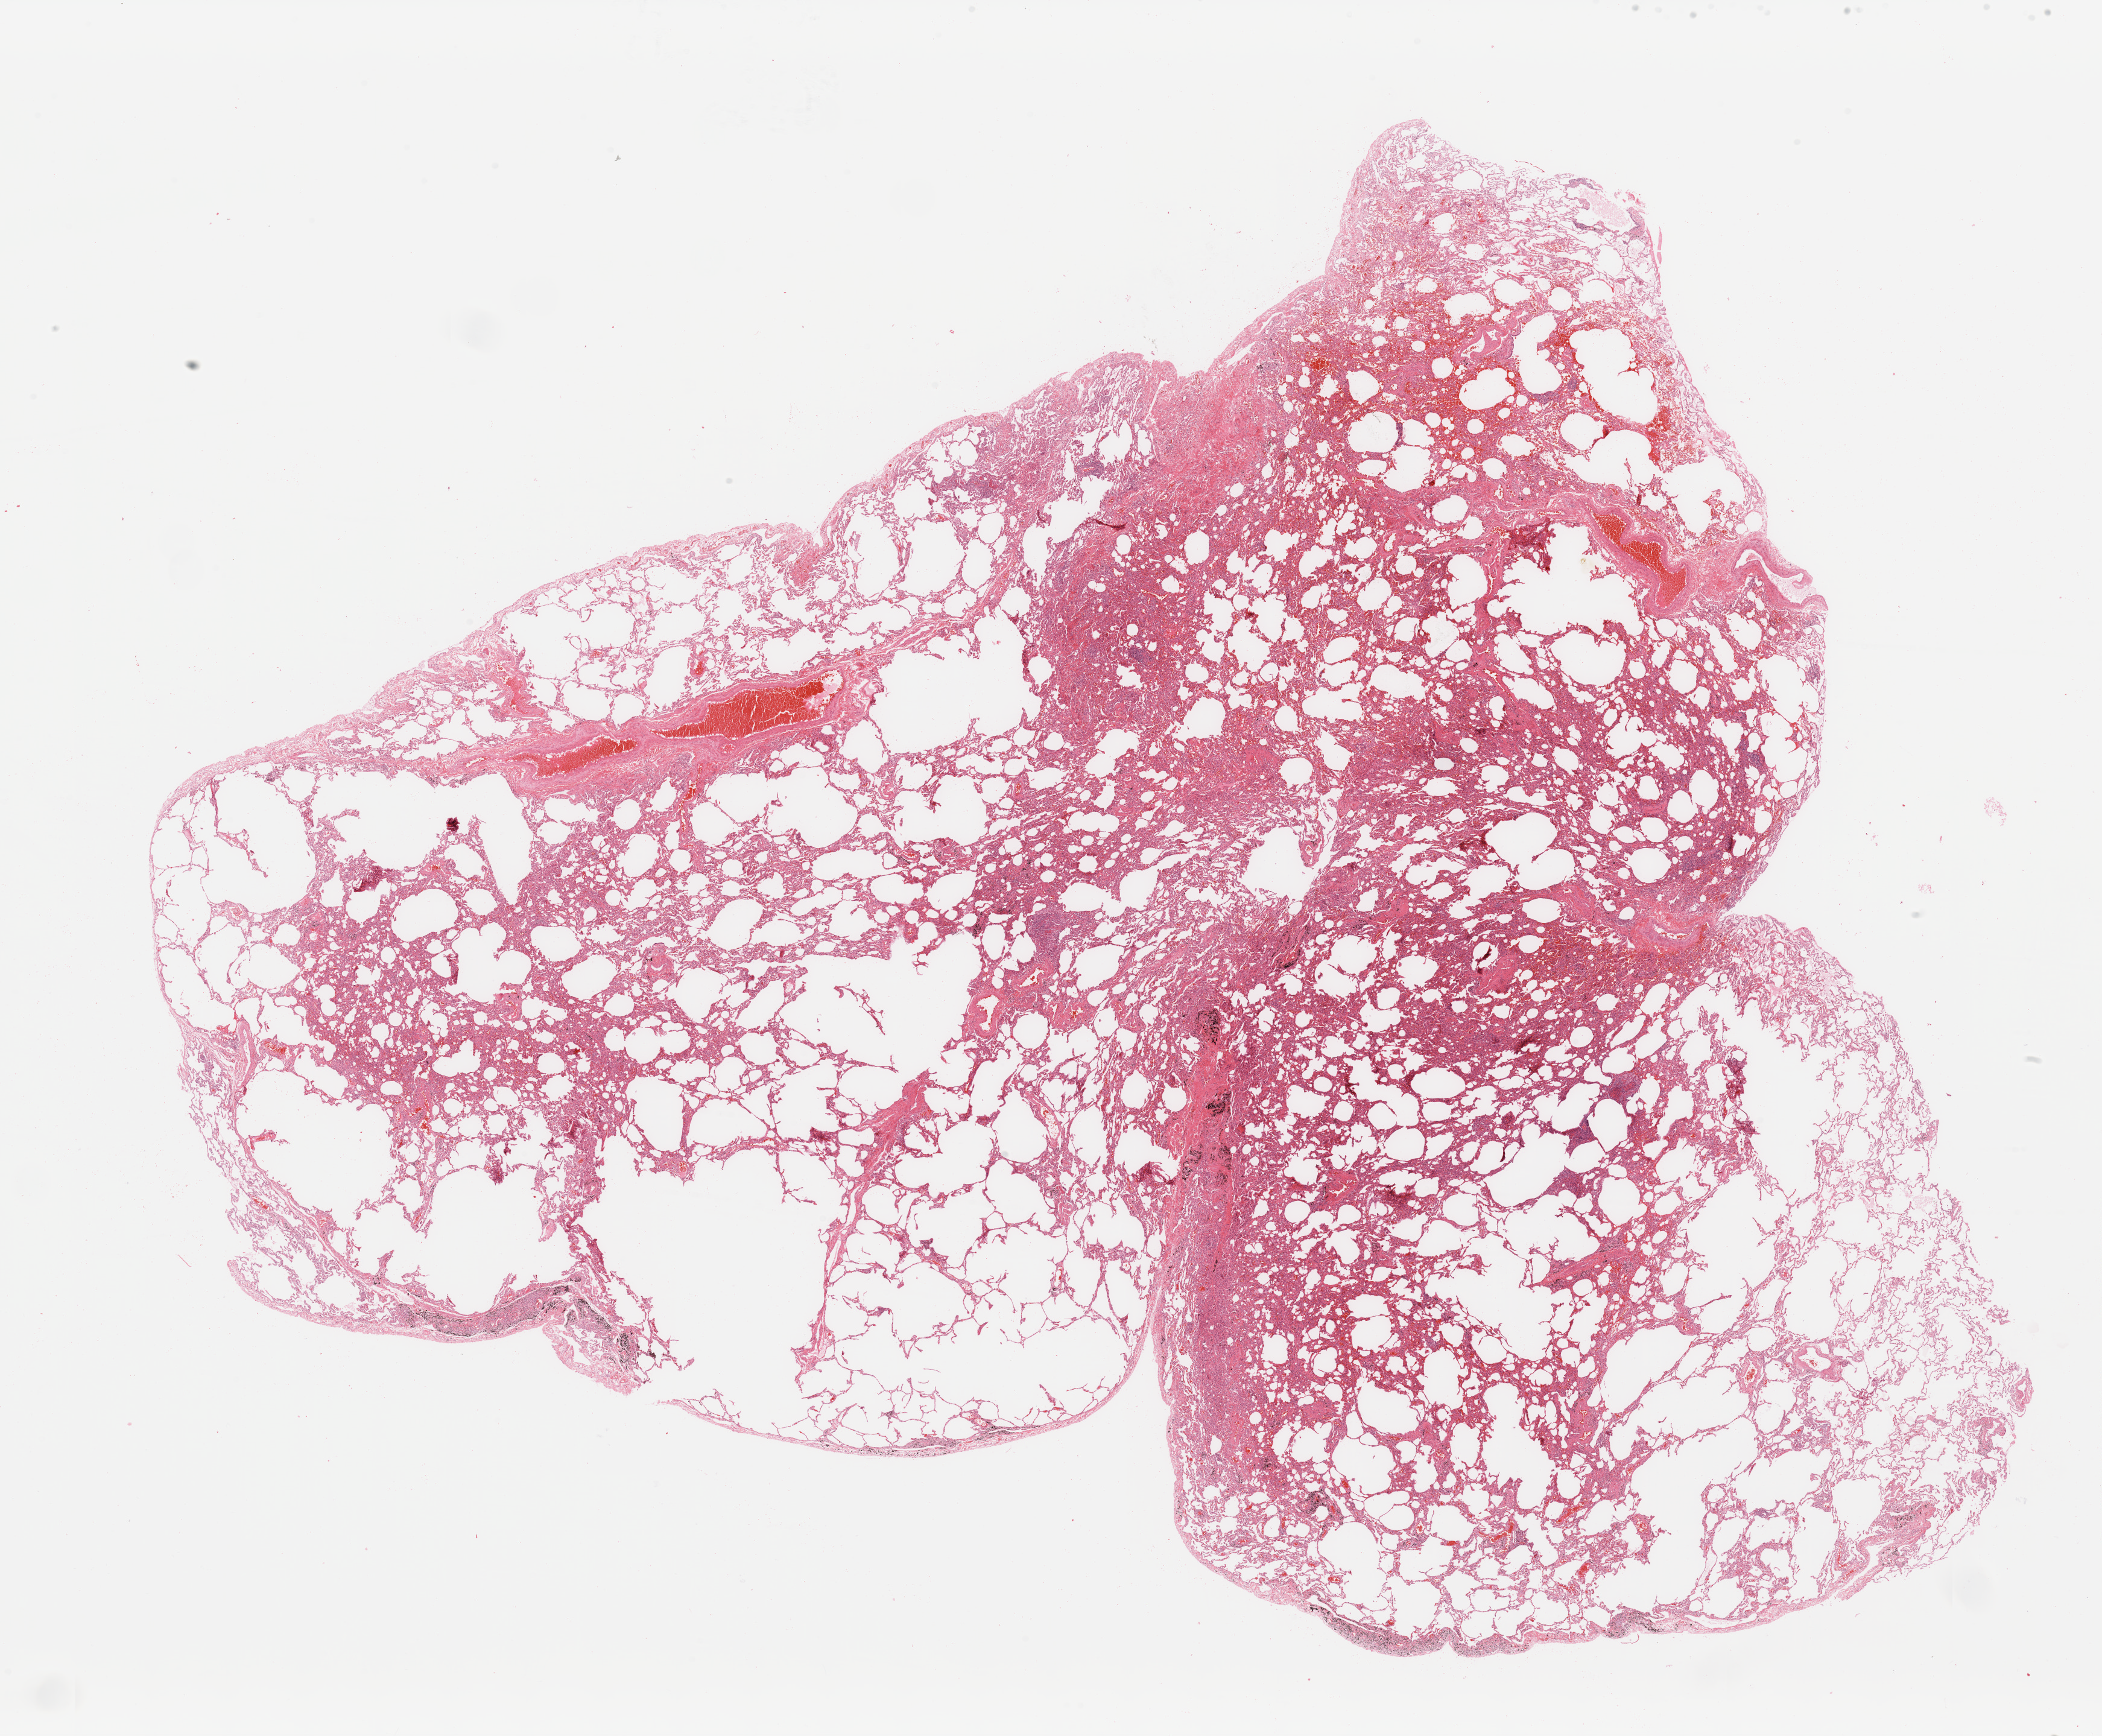
Whole-slide histology image, Hematoxylin and eosin (H&E) stained, whole scanned area (about 27.6 x 22.8 mm) shown as a low-resolution overview; normal (non-tumour) tissue sample, lung. Patient: female, age 66 years.
This section: normal (non-tumour) tissue from the same patient. Patient diagnosis: Adenocarcinoma, NOS.